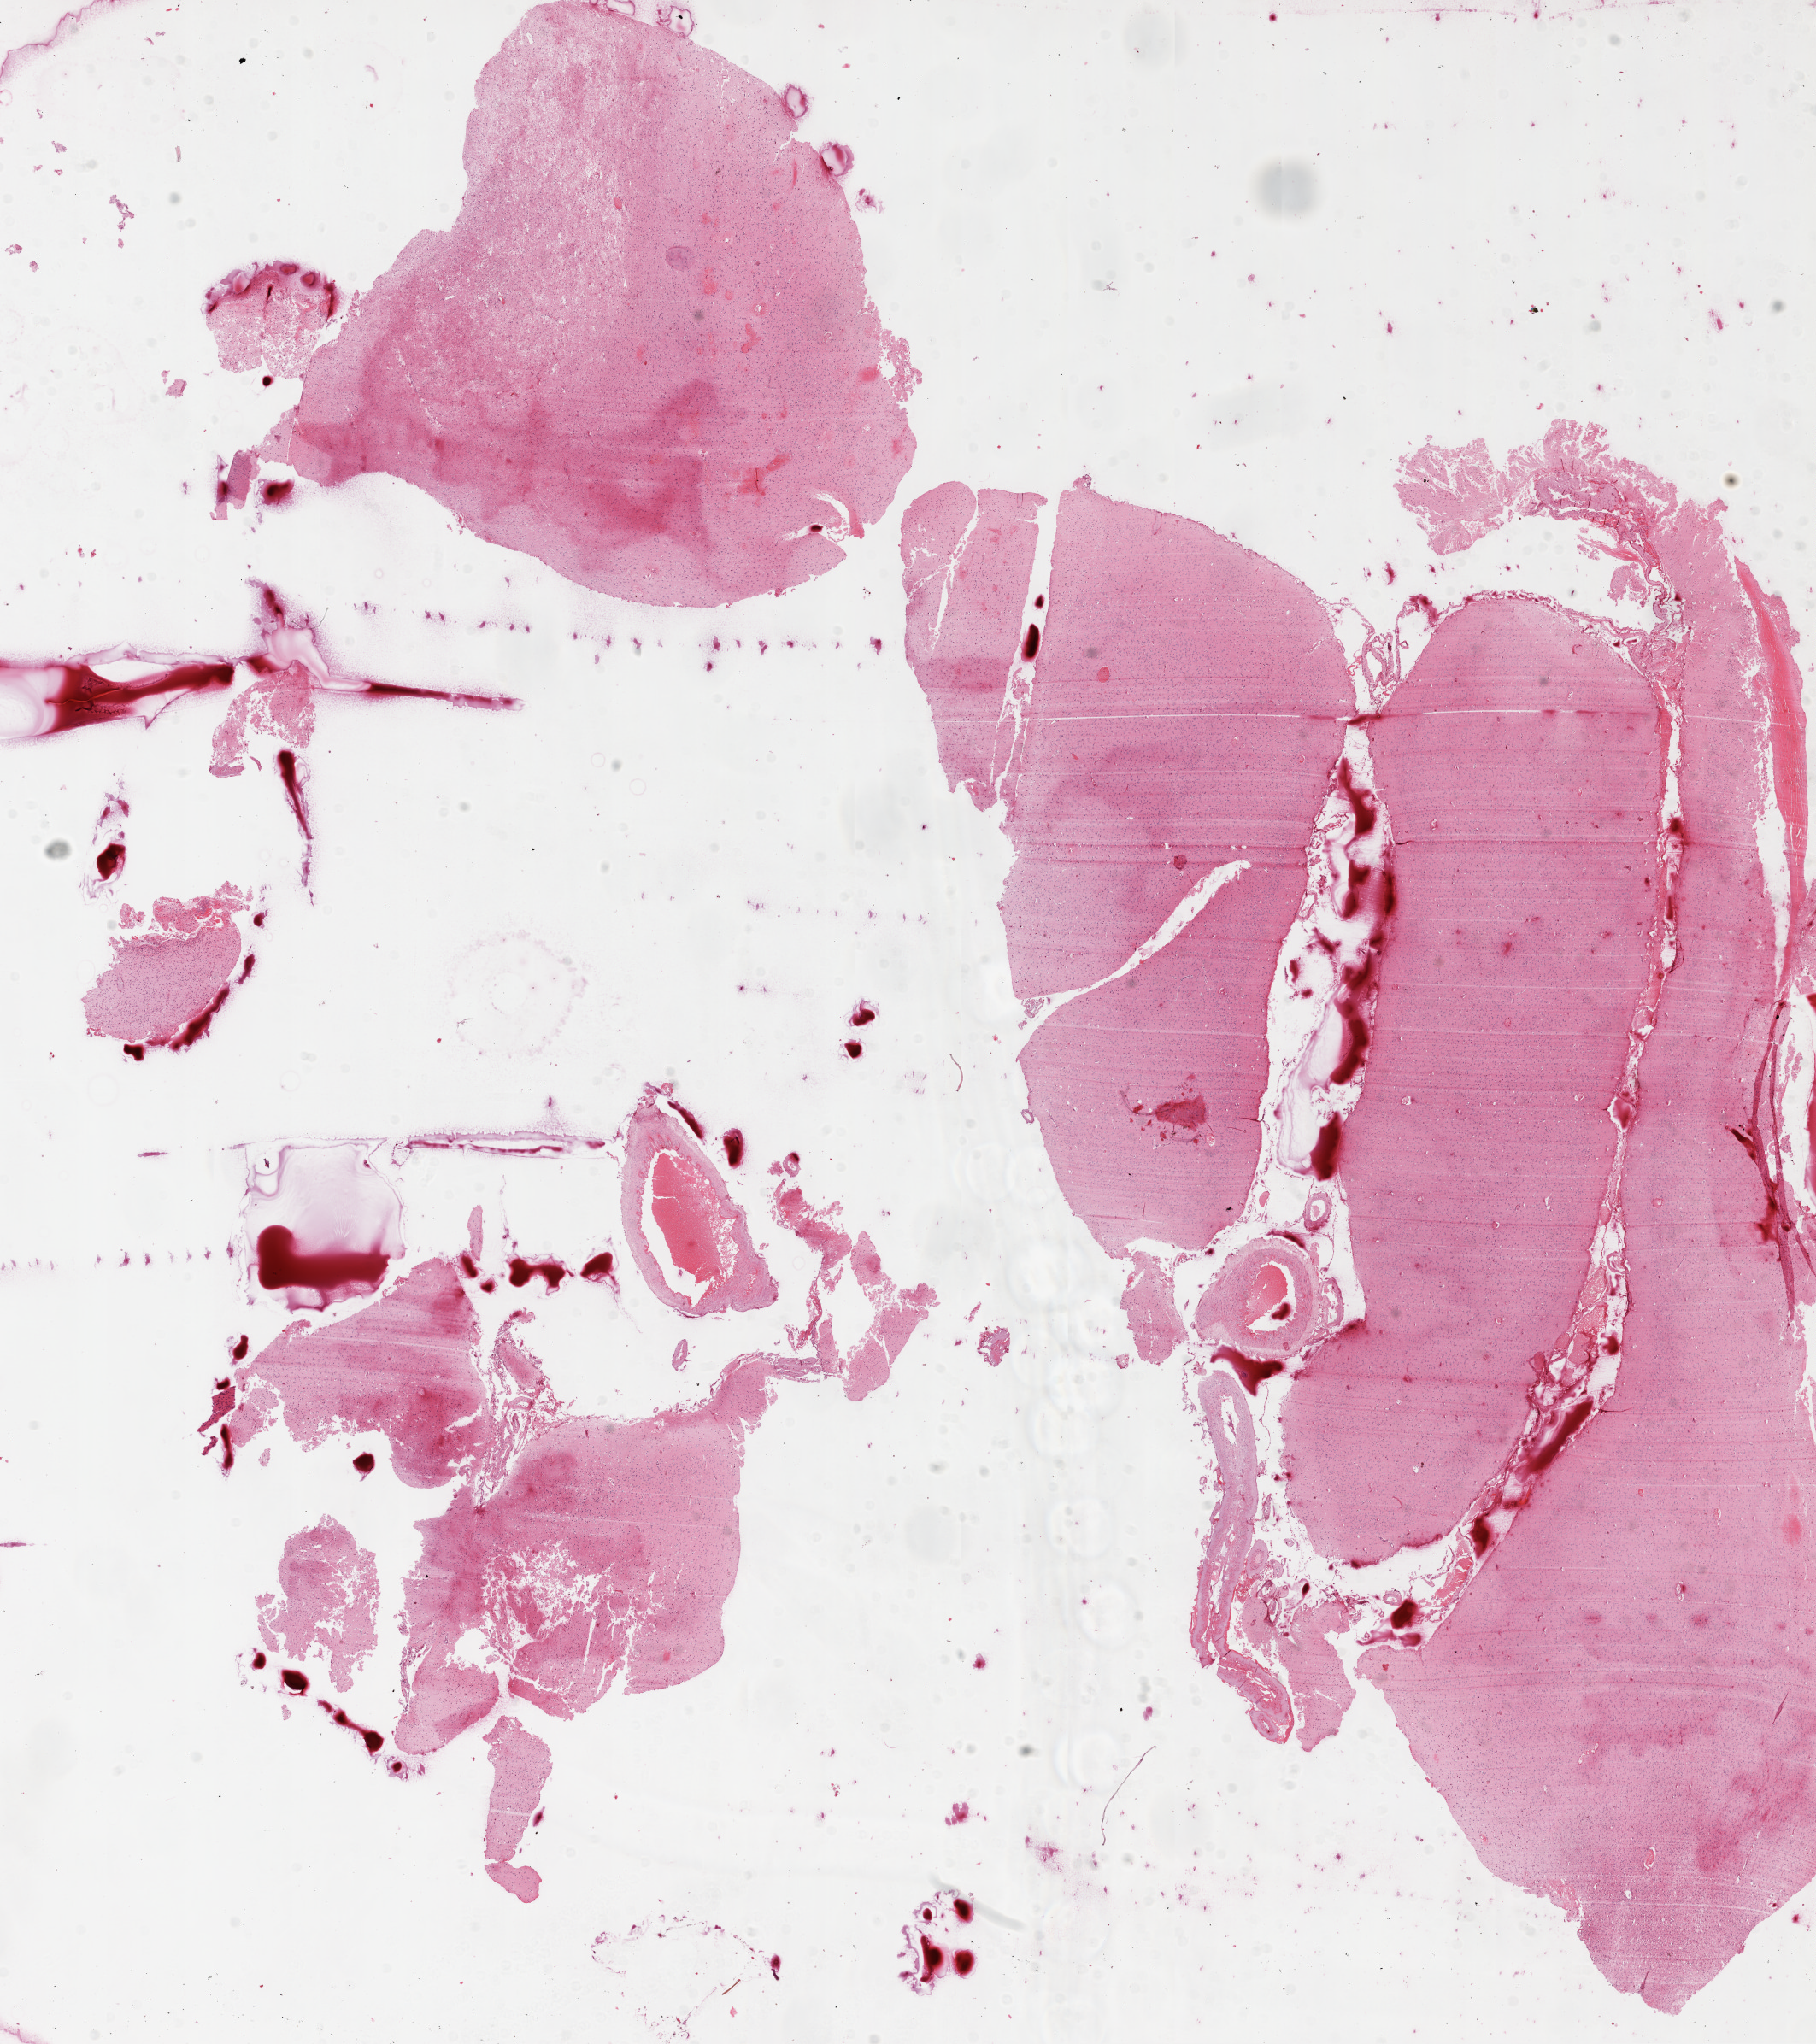
Digitized H&E-stained tissue section (whole slide), whole scanned area (about 17.1 x 19.2 mm, acquisition: 20x scan) shown as a low-resolution overview; formalin-fixed paraffin-embedded (FFPE) diagnostic section; brain, primary tumour sample. Male, age 66 years at initial diagnosis.
Pathologic diagnosis: Glioblastoma.